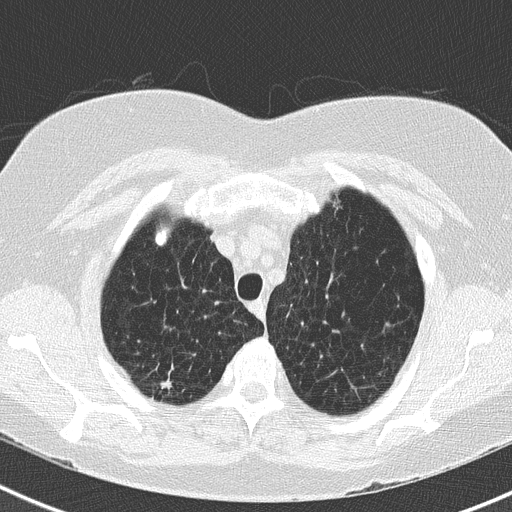
Axial slice from a low-dose chest CT screening exam; second screening round (one year after baseline); lung window (W 1500 / L -600 HU); 2 mm slice thickness; lung (sharp) reconstruction kernel (B50f); slice 37 of 183 in the series. Female participant, aged 73 years at enrolment. Former smoker at enrolment.
Expert-annotated lung lesion, box from (x=142, y=364) to (x=191, y=402) px. The screening reader recorded 2 non-calcified nodules or masses ≥4 mm on this exam (right upper lobe, right upper lobe); which of them this box marks is not recorded. Lung cancer was diagnosed 250 days after this screen: adenocarcinoma, NOS, right upper lobe, moderately differentiated (G2), stage IB (AJCC 6th edition), 15 mm at pathology.